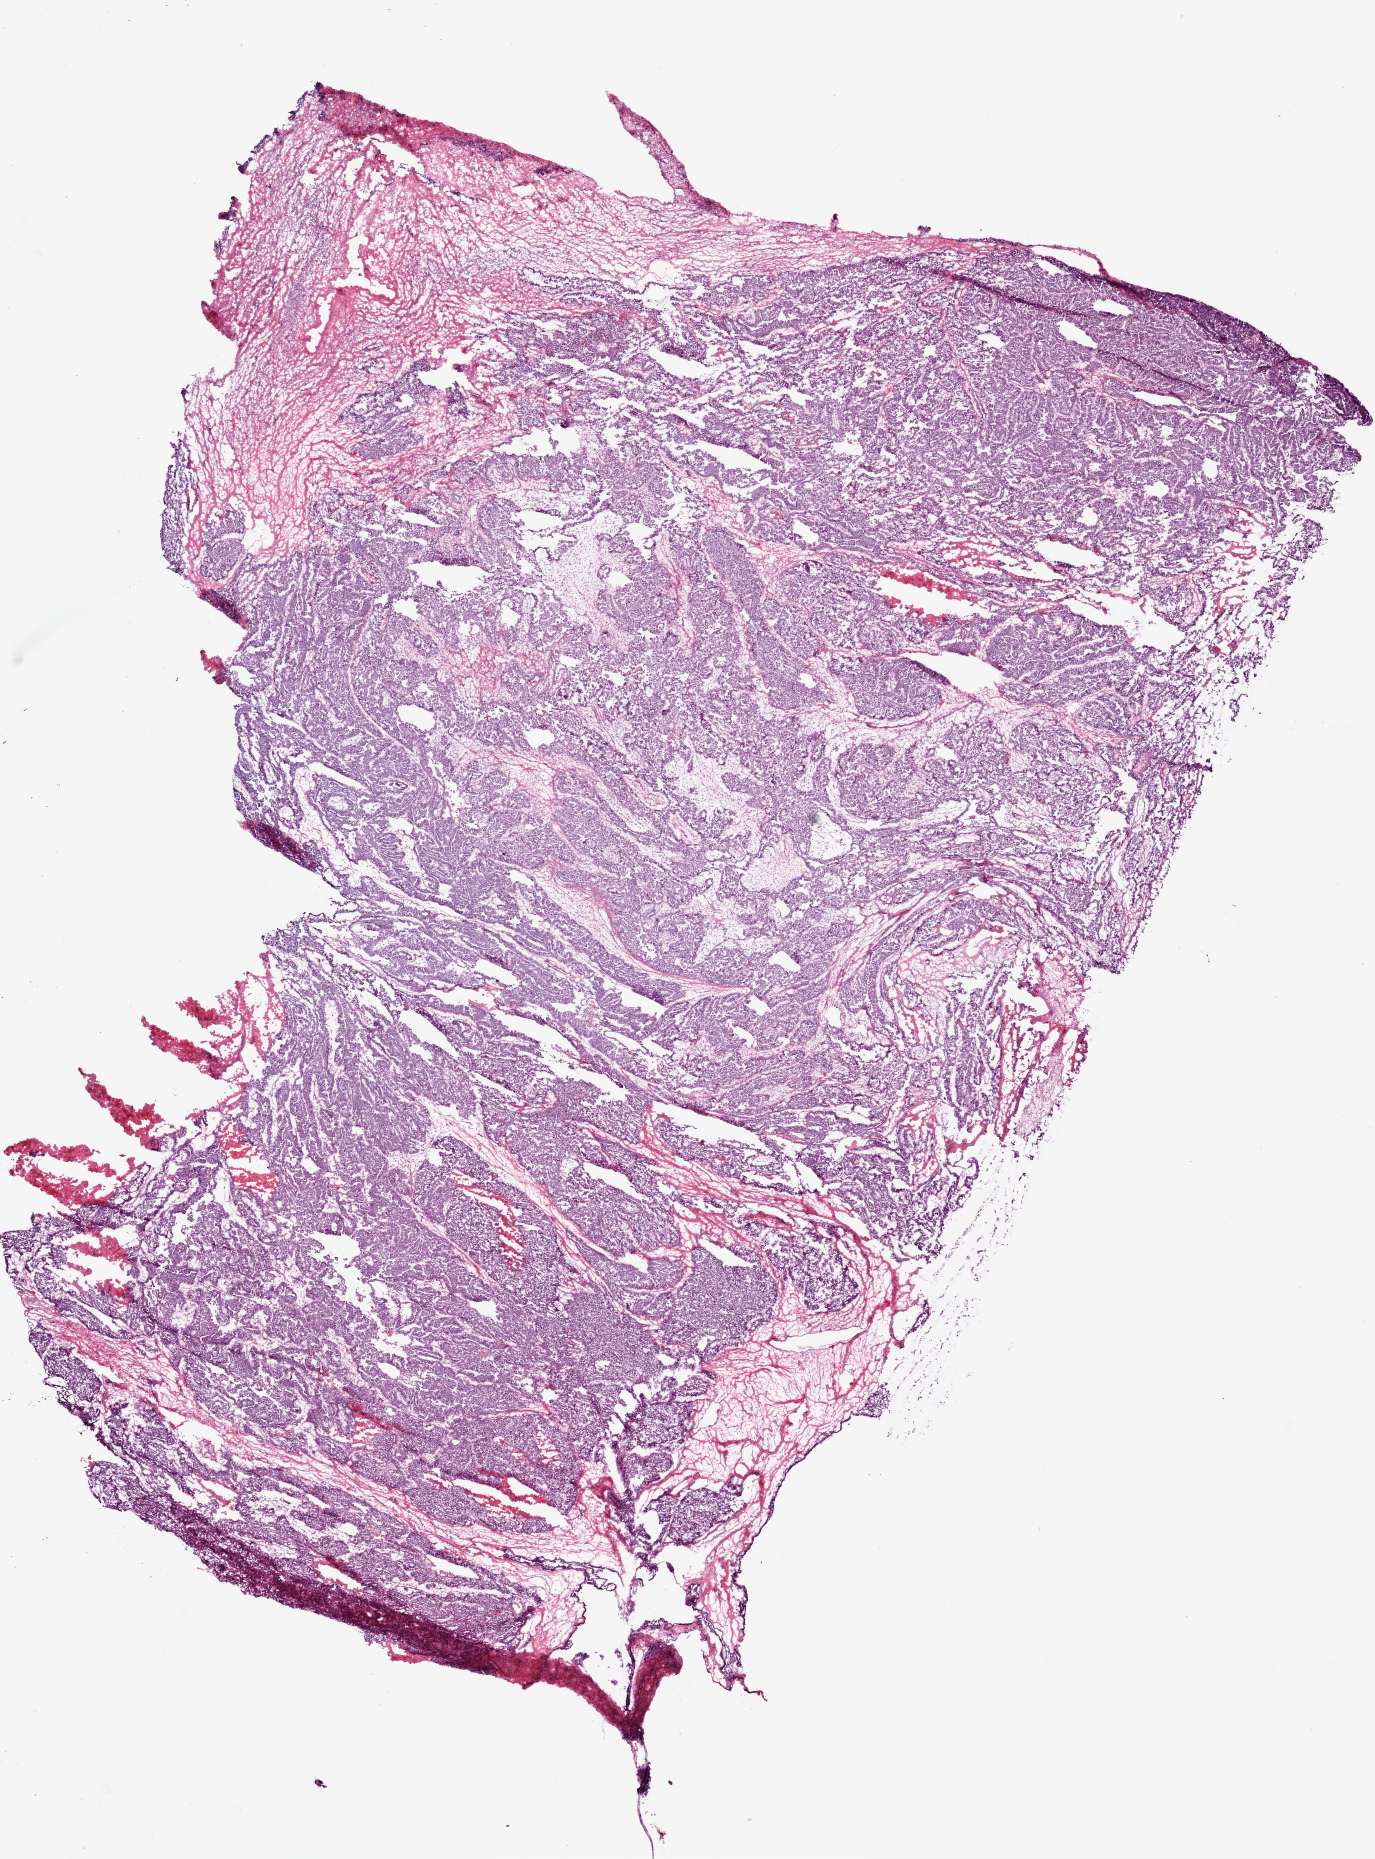
Digitized H&E-stained tissue section (whole slide), shown as a low-resolution overview of the whole scanned area (about 11.0 x 14.9 mm, slide scanned at 20x), frozen section from the bottom of the tissue portion, primary tumour sample from the ovary. Patient: female, age at initial diagnosis 49 years.
Histologic diagnosis: Serous cystadenocarcinoma, NOS.